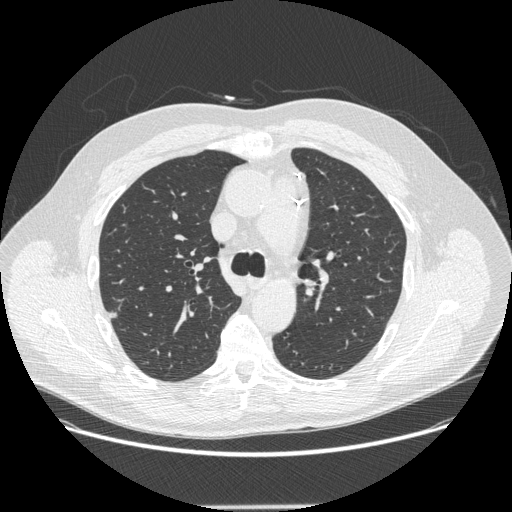
Chest CT (low-dose screening protocol), one axial image; third screening round (two years after baseline); lung window (W 1500 / L -600 HU); standard (soft-tissue) reconstruction kernel (STANDARD); 120 kVp; slice 75 of 265 in the series. Male participant, aged 62 years at enrolment.
Lesion marked by an expert reader, box from (x=94, y=297) to (x=134, y=337) px. Screening reader's record for this exam (one nodule recorded; not confirmed to be the boxed lesion): non-calcified nodule or mass ≥4 mm, right upper lobe, 12 × 11 mm, smooth margins, soft tissue attenuation, pre-existing on the prior screen: yes; interval growth: yes. Later outcome: lung cancer diagnosed 112 days after this screen — adenocarcinoma, NOS, right upper lobe, moderately differentiated (G2), stage IA (AJCC 6th edition), 12 mm at pathology.